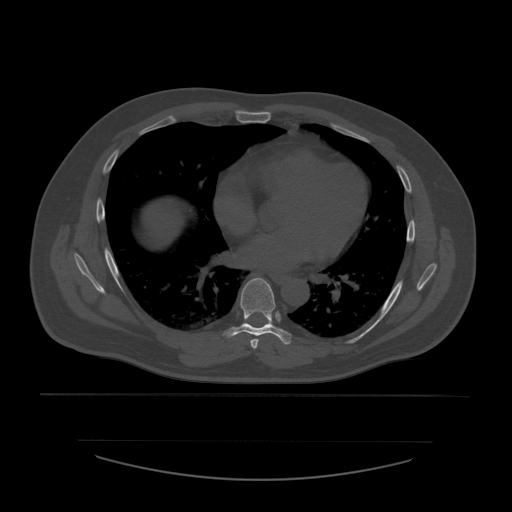
CT including the spine, one axial slice. Slice 361 of 532 in the series (ordered by position). 120 kVp. Bone window (W 1800 / L 400 HU). 1.25 mm slice thickness. 512 × 512 image matrix, field of view 441 × 441 mm. Patient age 44 years. Case-level facts recorded for this patient, not image findings: primary cancer: soft tissue sarcoma.
Outlined on this slice (semi-automatic segmentation, software-assisted and operator-edited):
- T6 vertebra: bounding box [x1, y1, x2, y2] px = [250, 339, 259, 349]
- T7 vertebra: [223, 278, 292, 345]